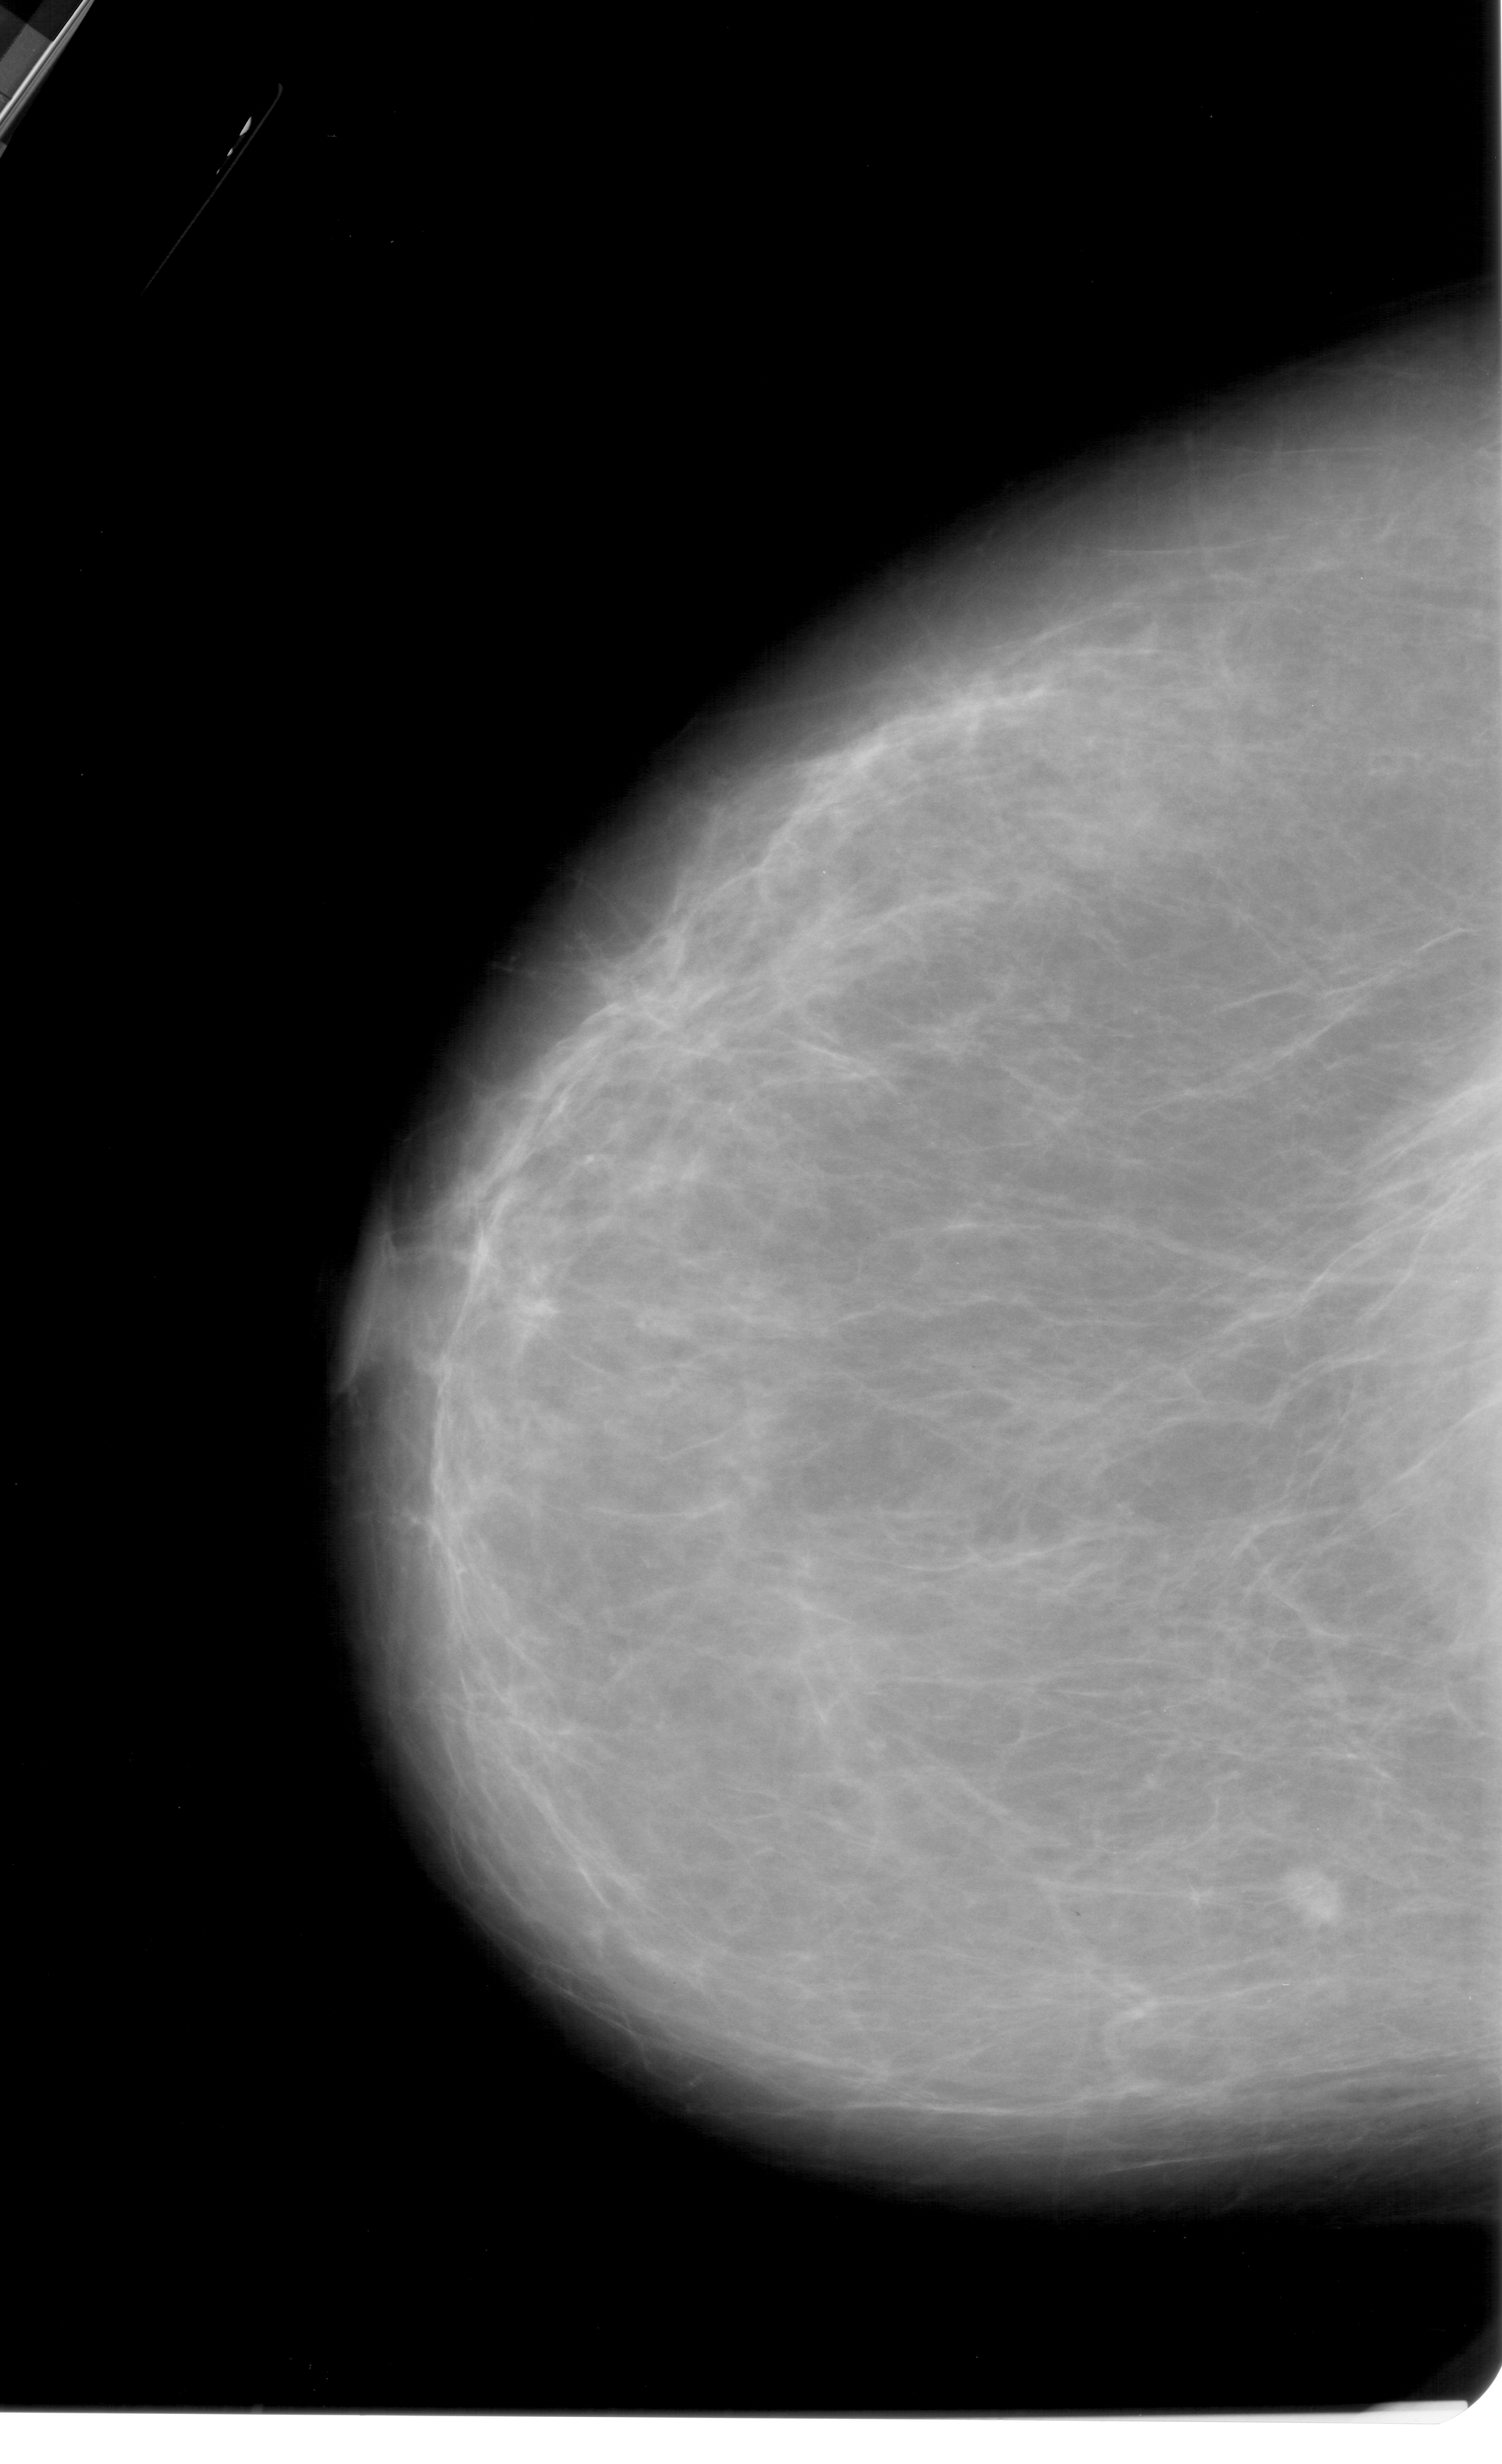
Scanned film-screen mammogram; left breast; craniocaudal (CC) view.
Marked findings (only marked abnormalities are described; nothing is implied about the rest of the image): mass, shape oval, margins ill defined; BI-RADS assessment category 5; pathology (as recorded): malignant.